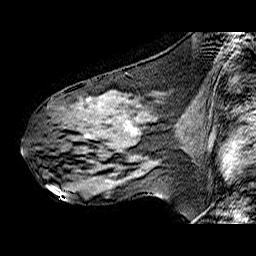
Breast MRI (dynamic contrast-enhanced), one sagittal slice. Slice 31 of 60 in the series (ordered by position). Dynamic contrast-enhanced series, time point 2 of 6 at this slice position (early post-contrast). 1.5 T. TE 6.3 ms, TR 32.9 ms. 4 mm slice thickness. 256 × 256 image matrix. Female patient. From the clinical record (not read from this slice): setting: breast cancer imaged before/during neoadjuvant chemotherapy; receptor status: HER2-positive.
Annotated regions visible in this slice (semi-automatic segmentation, software-assisted and operator-edited):
- analysis volume of interest (the breast-tissue region the enhancement analysis was run in; not a lesion): box from (x=47, y=91) to (x=167, y=173) px
- tumour enhancement mask (voxels above the 100 % enhancement threshold inside the analysis volume of interest): (x=87, y=125)–(x=137, y=137)